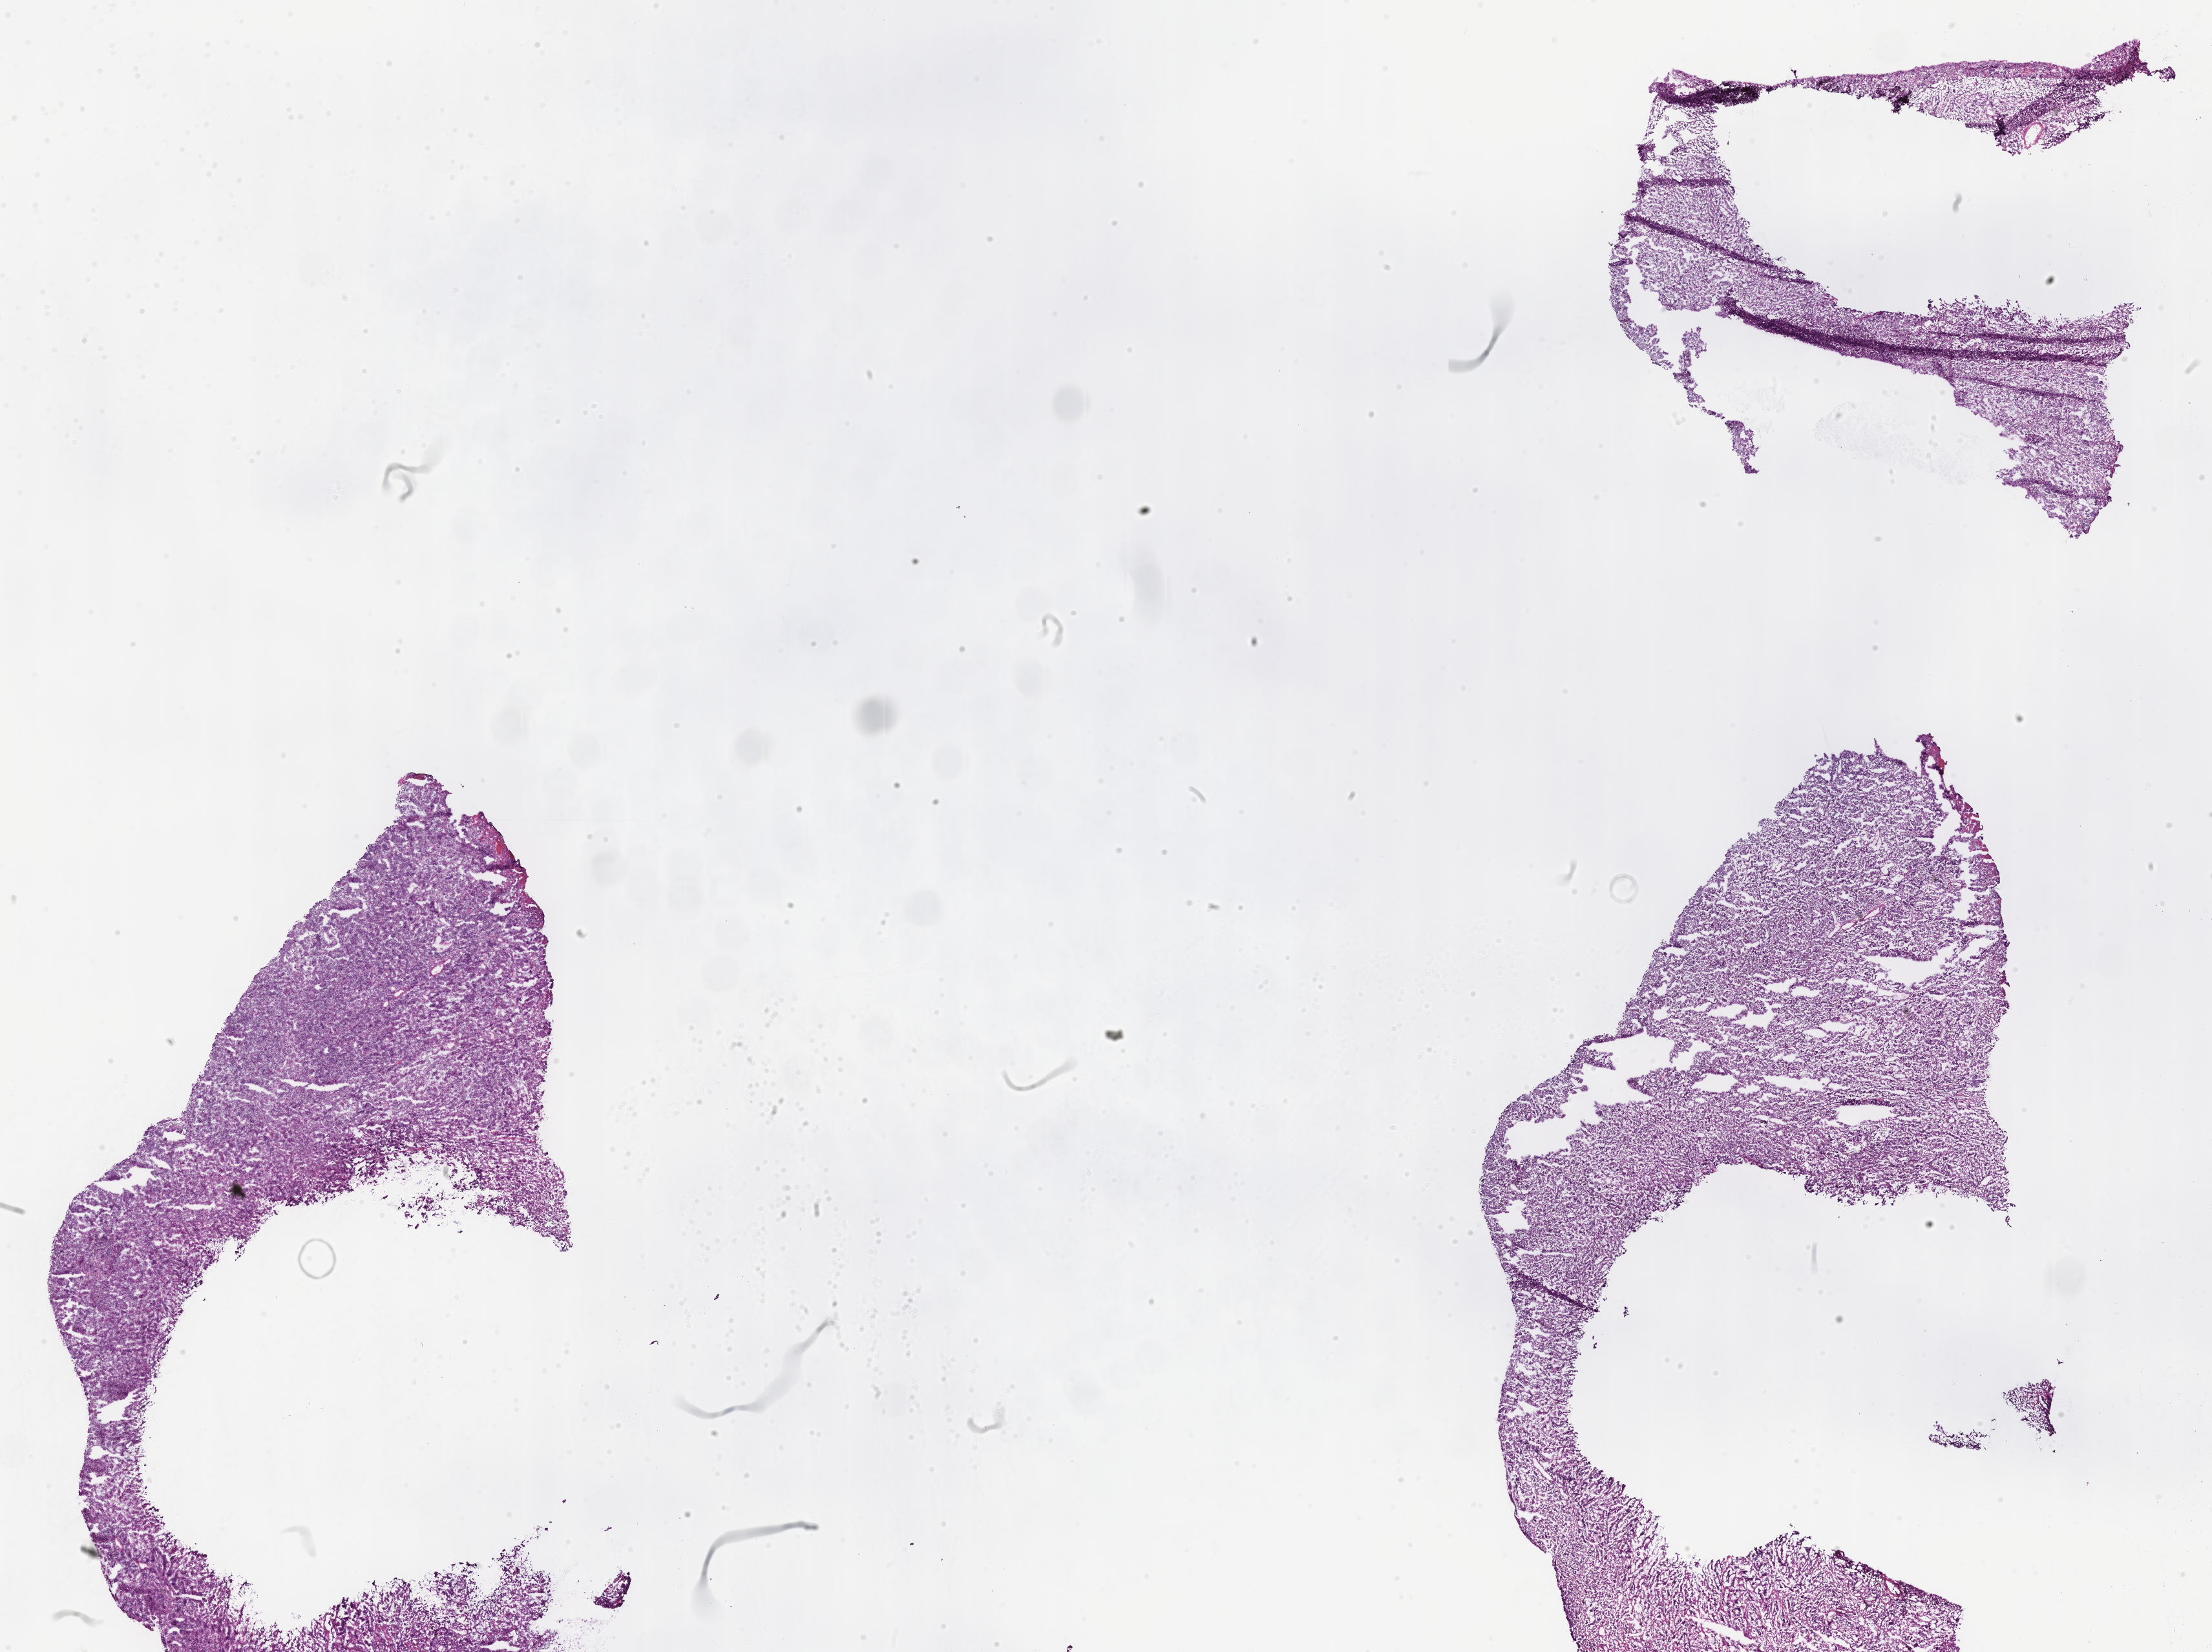
Haematoxylin and eosin whole-slide image — low-resolution overview of the scanned area, about 27.6 x 20.6 mm, cryosection, specimen: primary tumor, site: transverse colon. Patient: female, age at initial diagnosis 58 years. Tumor grade: G4 (undifferentiated). Pathologist review of this section (percent, as recorded): tumor cells 65%, tumor nuclei 65%, stromal cells 10%, necrosis 0%, normal cells 25%. Inflammatory infiltration, as recorded: lymphocyte infiltration 15%, monocyte infiltration 0%, neutrophil infiltration 10%.
* histologic diagnosis: Adenocarcinoma, metastatic, NOS
* AJCC pathologic stage: Stage IIB
* section: top of the tissue portion